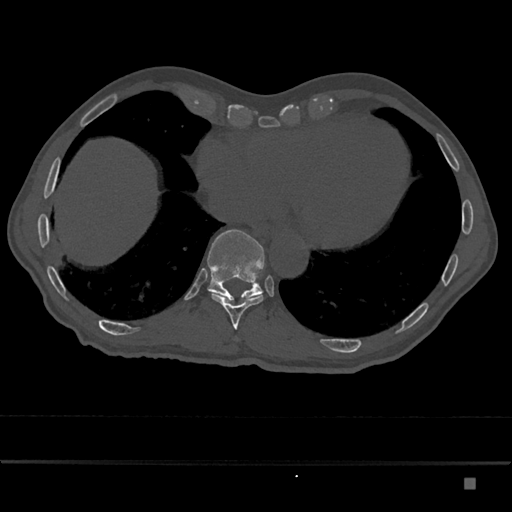
CT including the spine, one axial slice. Position 718 of 797 along the scan axis. Reconstruction kernel Br40s/3. 120 kVp. Bone window (W 1800 / L 400 HU). 512 × 512 image matrix, field of view 390 × 390 mm. Patient: male, 72 years. From the clinical record (not read from this slice): primary cancer: prostate.
Outlined on this slice (semi-automatically segmented with operator editing):
- T10 vertebra: box from (x=212, y=293) to (x=263, y=330) px
- T11 vertebra: (x=207, y=229)–(x=265, y=303)